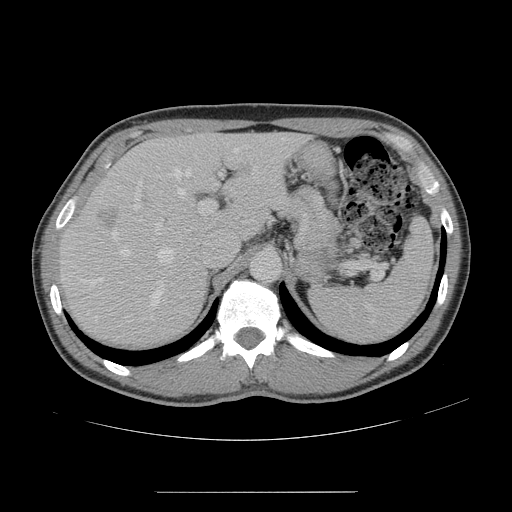
Contrast-enhanced abdominal CT, one axial slice; slice 104 of 178 in the series (ordered by position); 120 kVp; intravenous contrast given; soft-tissue window (W 400 / L 40 HU); 512 × 512 image matrix, field of view 401 × 401 mm. Male patient, age 53 years. Case-level facts recorded for this patient, not image findings: diagnosis: colorectal cancer liver metastases, imaged before liver resection; multiple liver metastases: yes; largest metastasis: 2.4 cm; disease in both lobes: no.
Annotated regions visible in this slice (manually delineated by an expert):
- hepatic veins: bounding box (x1, y1, x2, y2) in pixels: (91, 148, 255, 308)
- liver: (62, 134, 303, 344)
- planned liver remnant (the part of the liver to remain after resection): (148, 135, 303, 235)
- portal vein (with intrahepatic branches): (132, 181, 215, 235)
- liver metastasis: (99, 209, 121, 229)